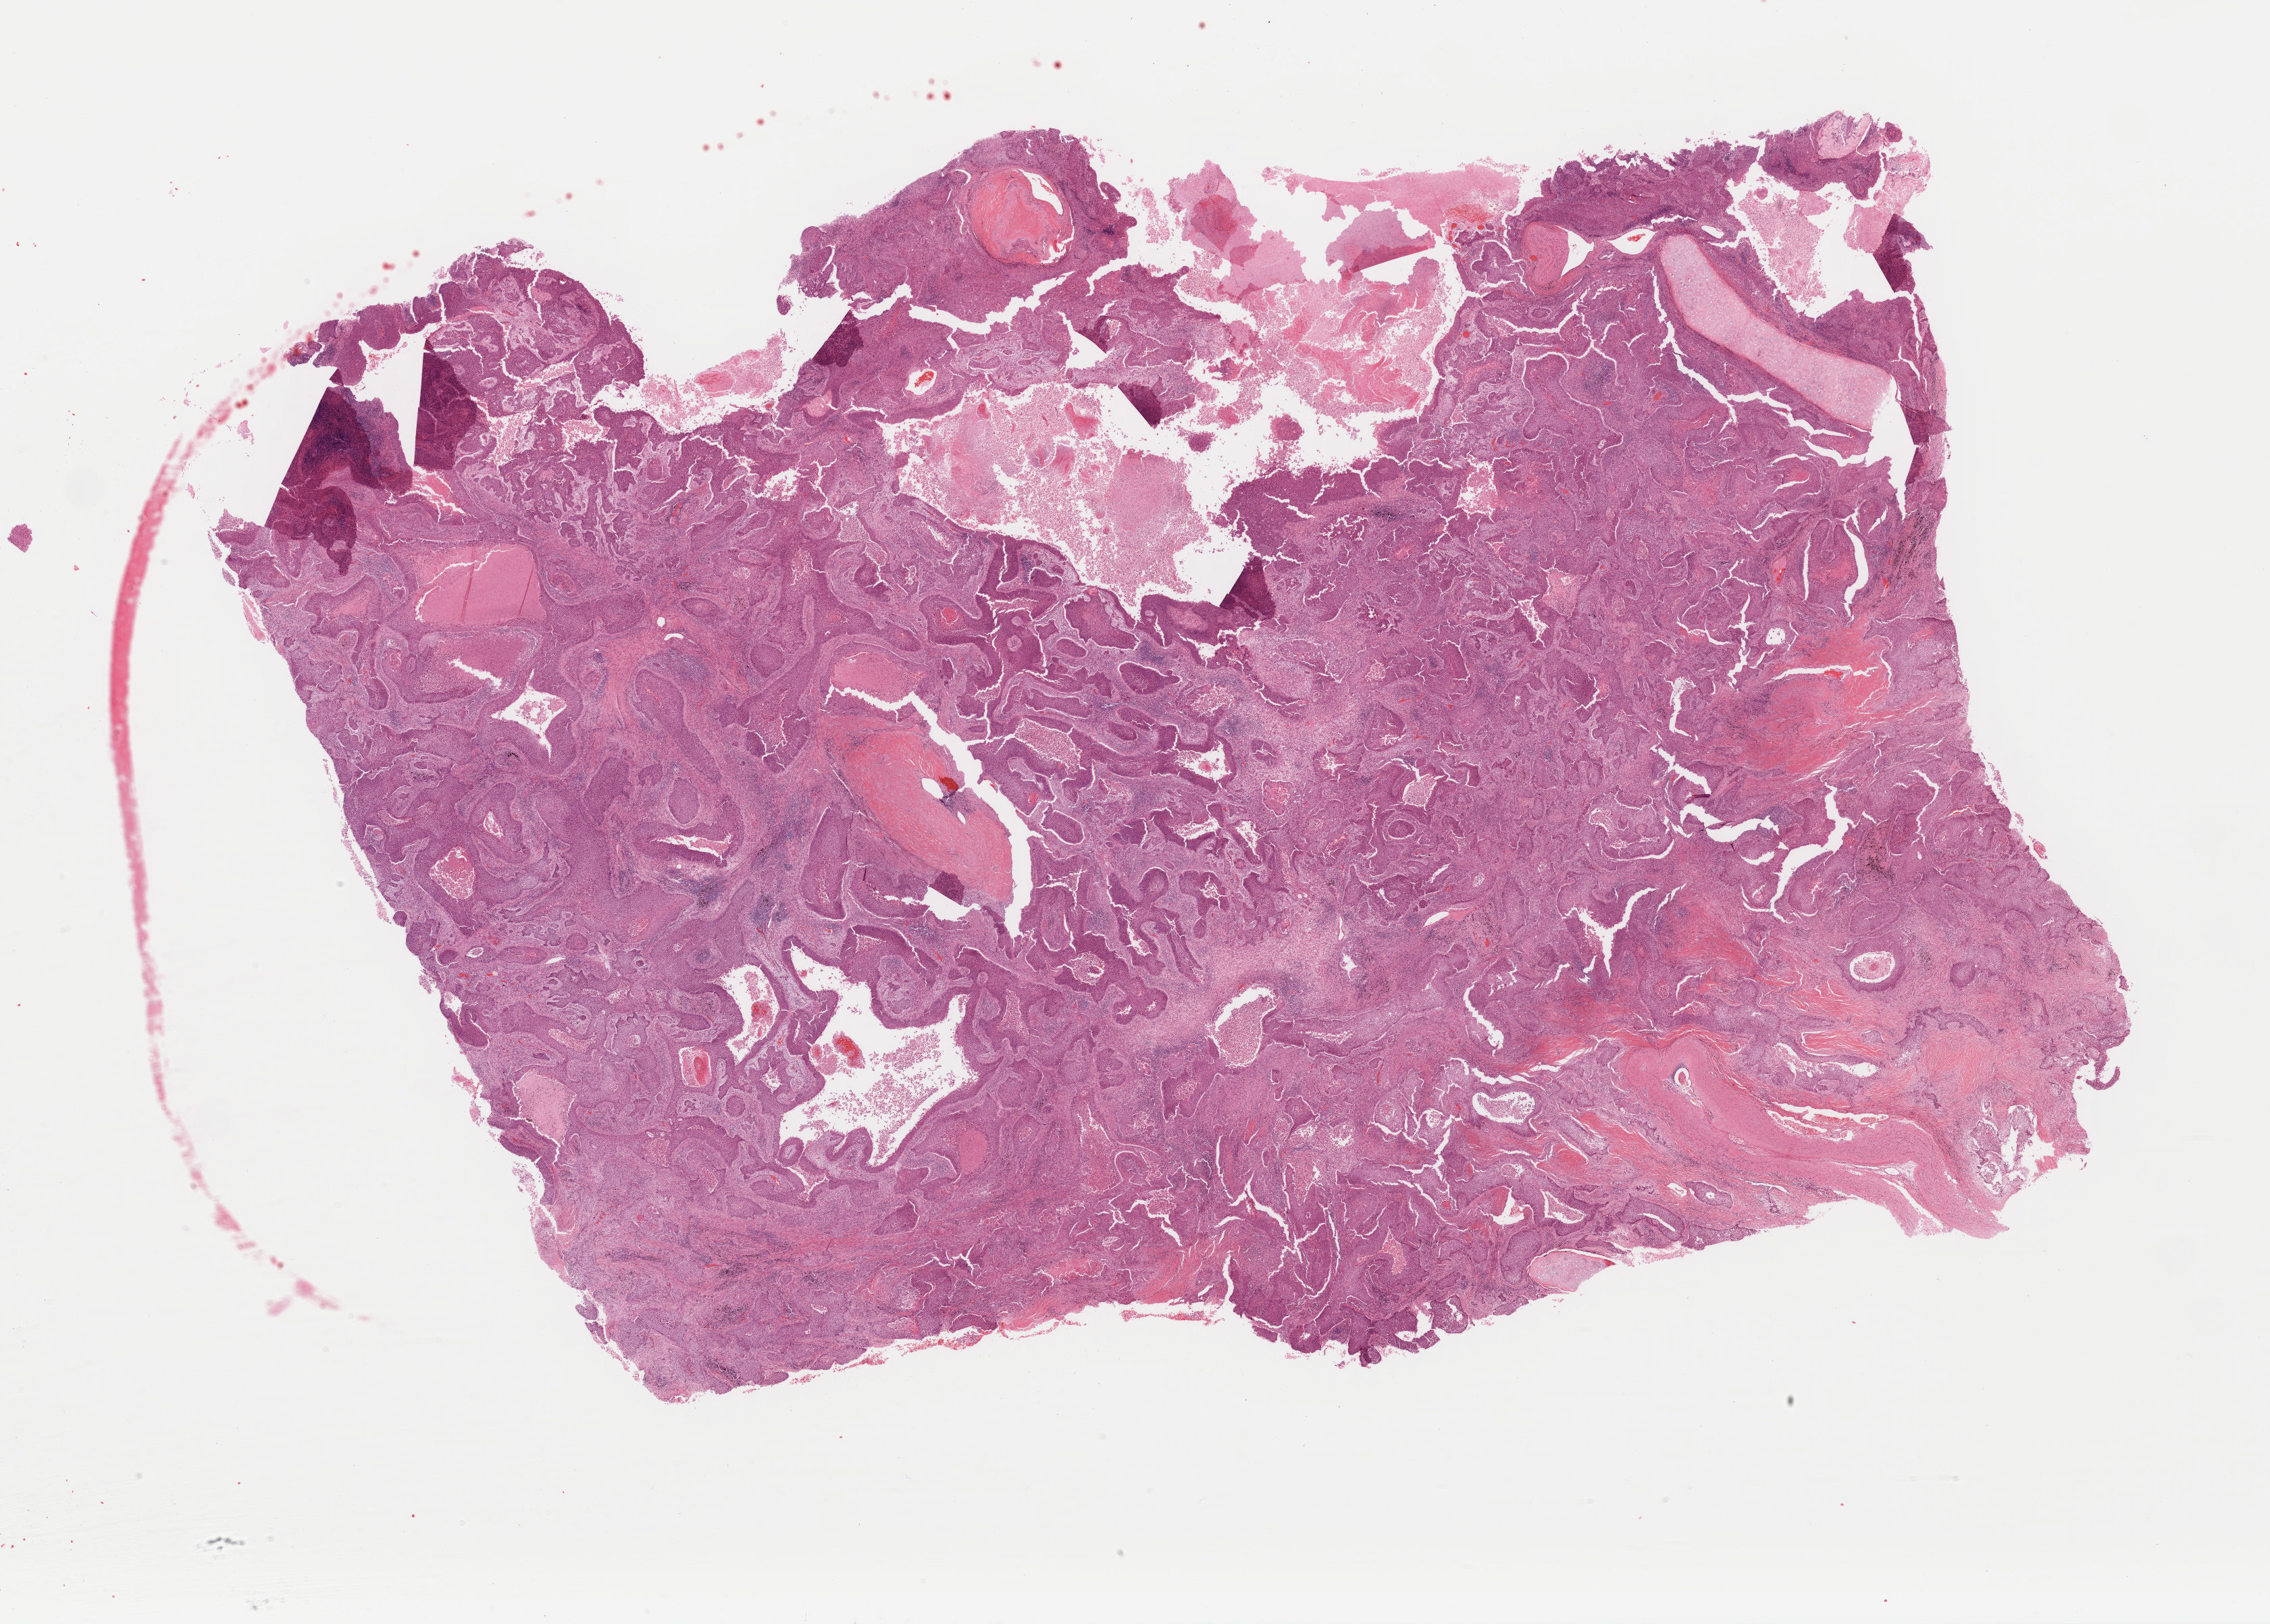
Whole-slide histology image, Hematoxylin and eosin (H&E) stained, whole scanned area (about 26.5 x 19.0 mm, acquisition: 40x scan) shown as a low-resolution overview, formalin-fixed paraffin-embedded (FFPE) diagnostic section, sample: primary tumour, lung. Female, age 56 years at initial diagnosis.
• diagnosis: Squamous cell carcinoma, NOS (lower lobe, lung)
• AJCC pathologic stage: IIB (7th edition)